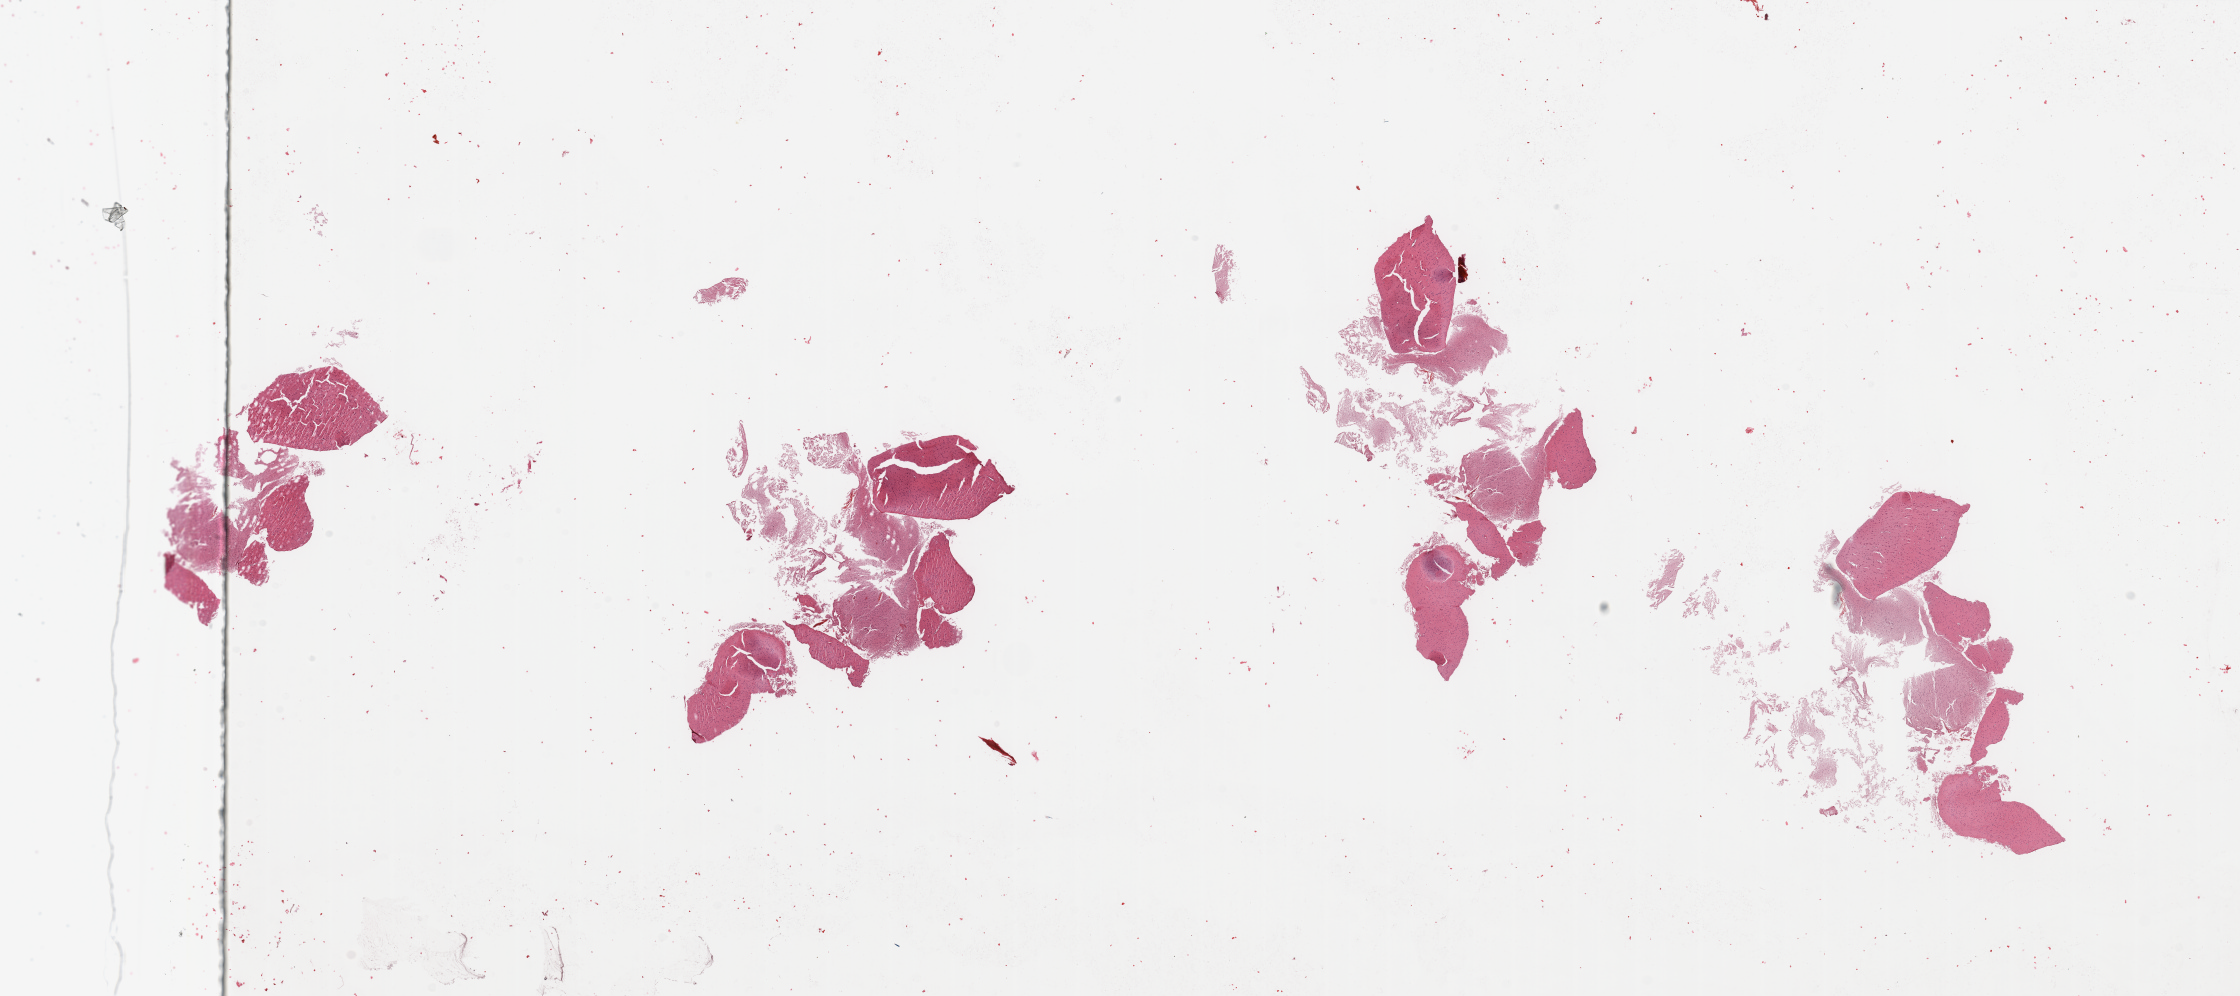
Hematoxylin and eosin (H&E) stained whole-slide image — a low-resolution overview of the entire scanned area, about 35.4 x 15.8 mm. Tumour tissue sample, brain. 73-year-old male patient.
- patient diagnosis (cohort enrolment): glioblastoma multiforme (brain)
- primary tumour site (as recorded): temporal lobe